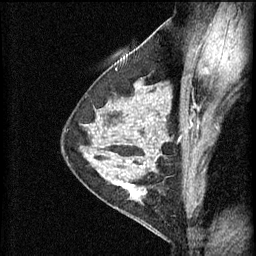
Breast MRI (dynamic contrast-enhanced), one sagittal slice; slice 39 of 60 in the series (ordered by position); 3 images stored at this slice position (order not interpretable as contrast timing); 1.5 T; TE 4.2 ms, TR 11 ms; 256 × 256 image matrix, field of view 180 × 180 mm. Female patient, age 29 years.
Structures marked on this image (semi-automatically segmented with operator editing):
- analysis volume of interest (the breast-tissue region the enhancement analysis was run in; not a lesion): bounding box <105,172,166,227> (left, top, right, bottom; pixels)
- tumour enhancement mask (voxels above the 70 % enhancement threshold inside the analysis volume of interest): <113,172,147,199>